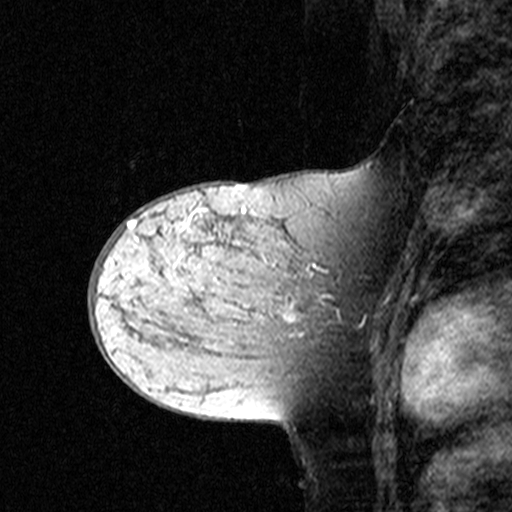
Breast MRI (dynamic contrast-enhanced), one sagittal slice; slice 21 of 44 in the series (ordered by position); dynamic contrast-enhanced study with each time point stored as its own series, time point 2 of 3 at this slice position (early post-contrast, ordered by acquisition time); 1.5 T; TE 4.5 ms, TR 11 ms; 3 mm slice thickness; 512 × 512 image matrix. Female patient, age 44 years. Case-level facts recorded for this patient, not image findings: setting: breast cancer imaged before/during neoadjuvant chemotherapy; receptor status: triple-negative.
Outlined on this slice (semi-automatically segmented with operator editing):
- analysis volume of interest (the breast-tissue region the enhancement analysis was run in; not a lesion): bounding box [x1, y1, x2, y2] px = [142, 208, 349, 363]
- tumour enhancement mask (voxels above the 90 % enhancement threshold inside the analysis volume of interest): [247, 302, 339, 322]